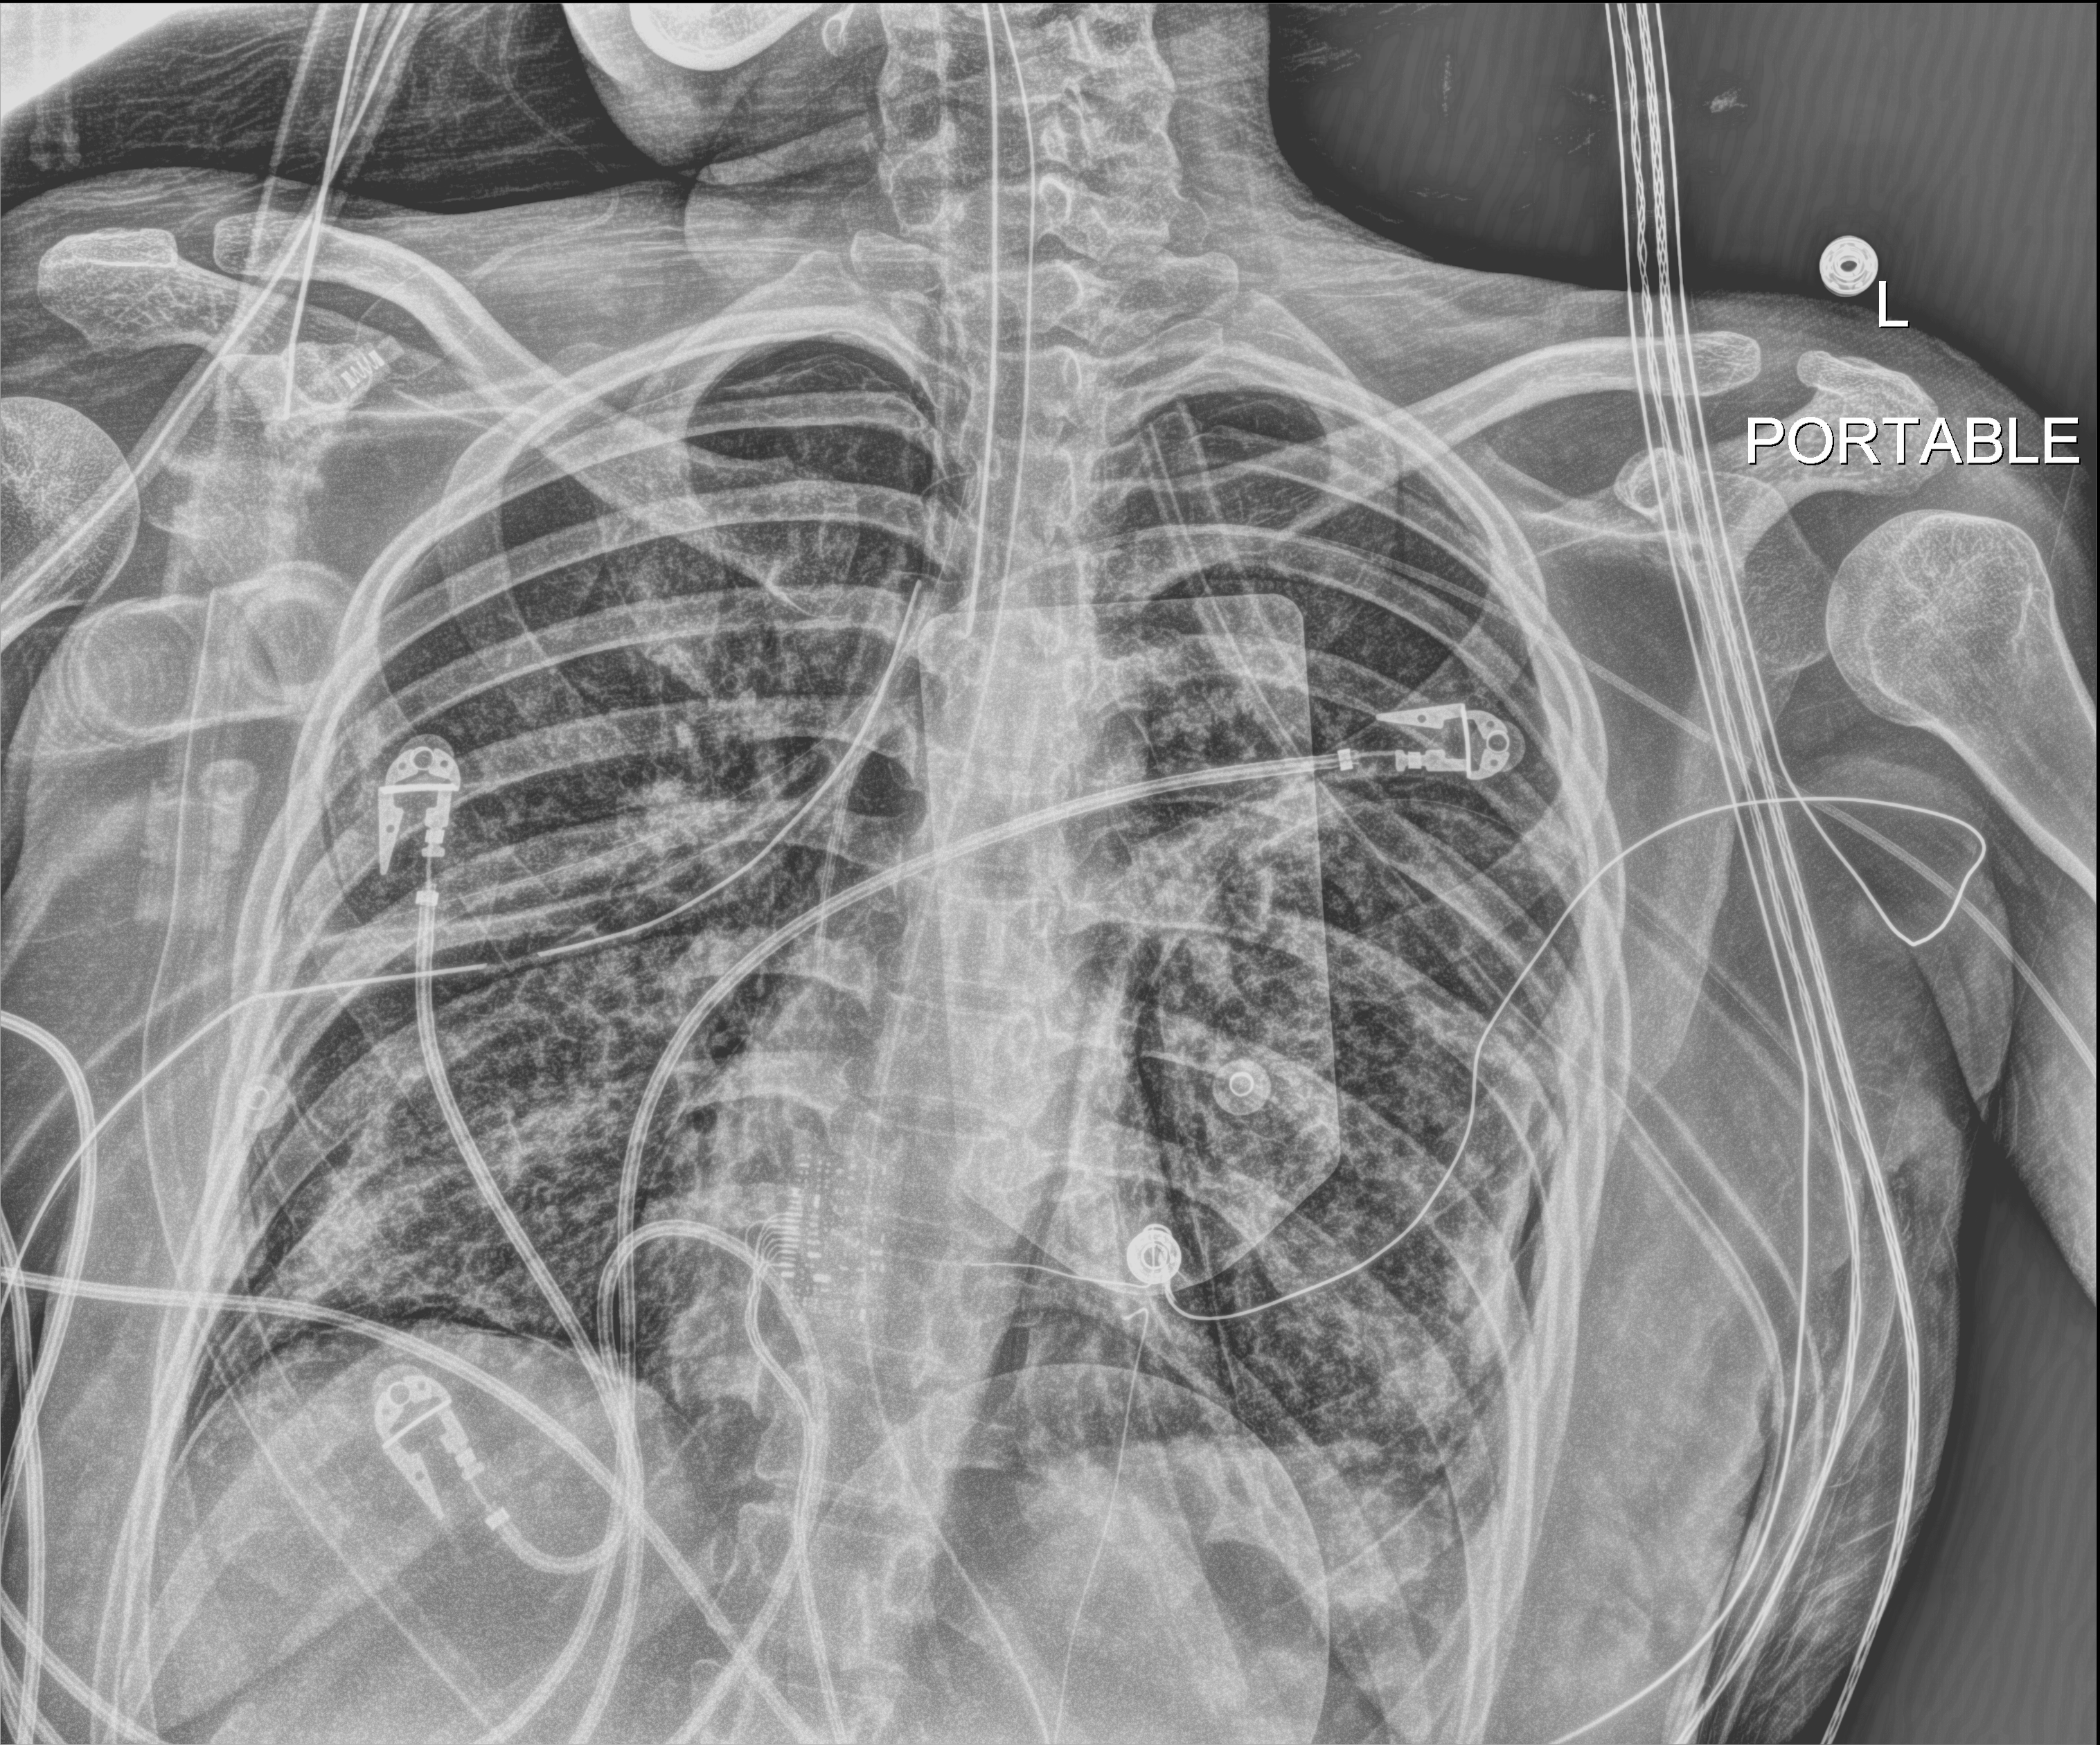
Bedside chest radiograph (digital radiography). Patient hospitalised with COVID-19, aged 18–59 years.
Admission-level facts for this patient (not findings on this image; timing relative to this image not recorded): diabetes (admission record): no; hypertension (admission record): no; admitted to intensive care during this hospital stay: yes.